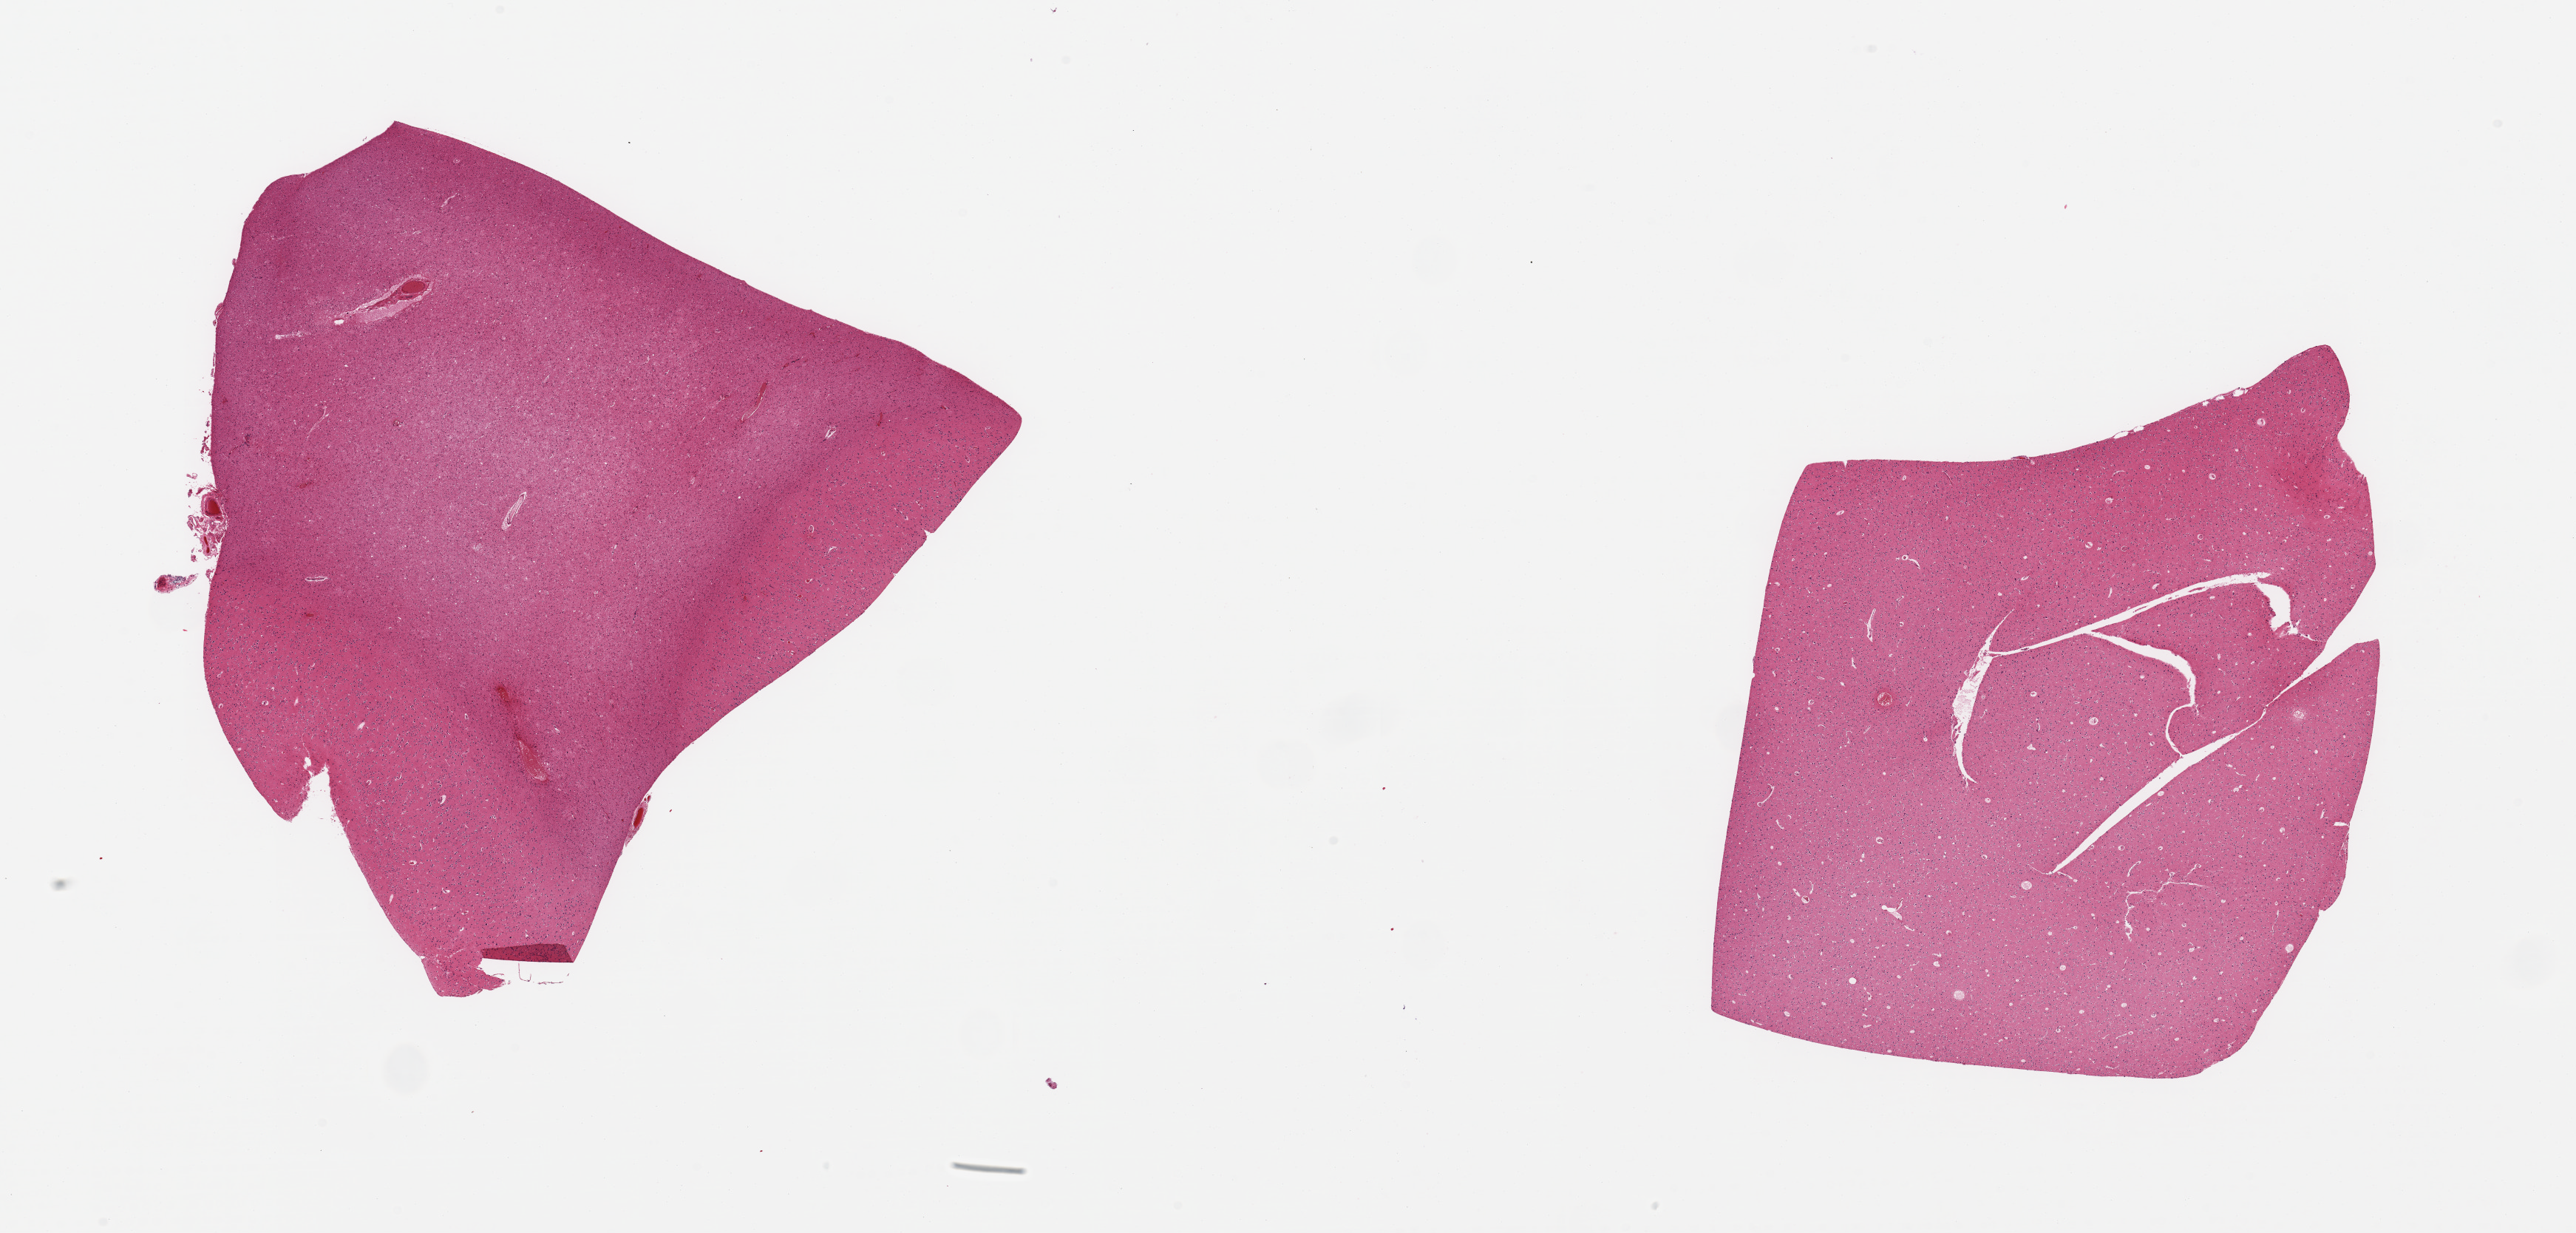
Digitized haematoxylin and eosin-stained section, brightfield, shown as a low-resolution overview of the whole scanned area (about 27.6 x 13.2 mm, slide scanned at 20x); PAXgene-fixed, paraffin-embedded tissue; section of cerebral cortex (target tissue); donor tissue sample. Donor sex: male.
* pathologist's review note for this sample: 2 pieces; 1 is largely white matter